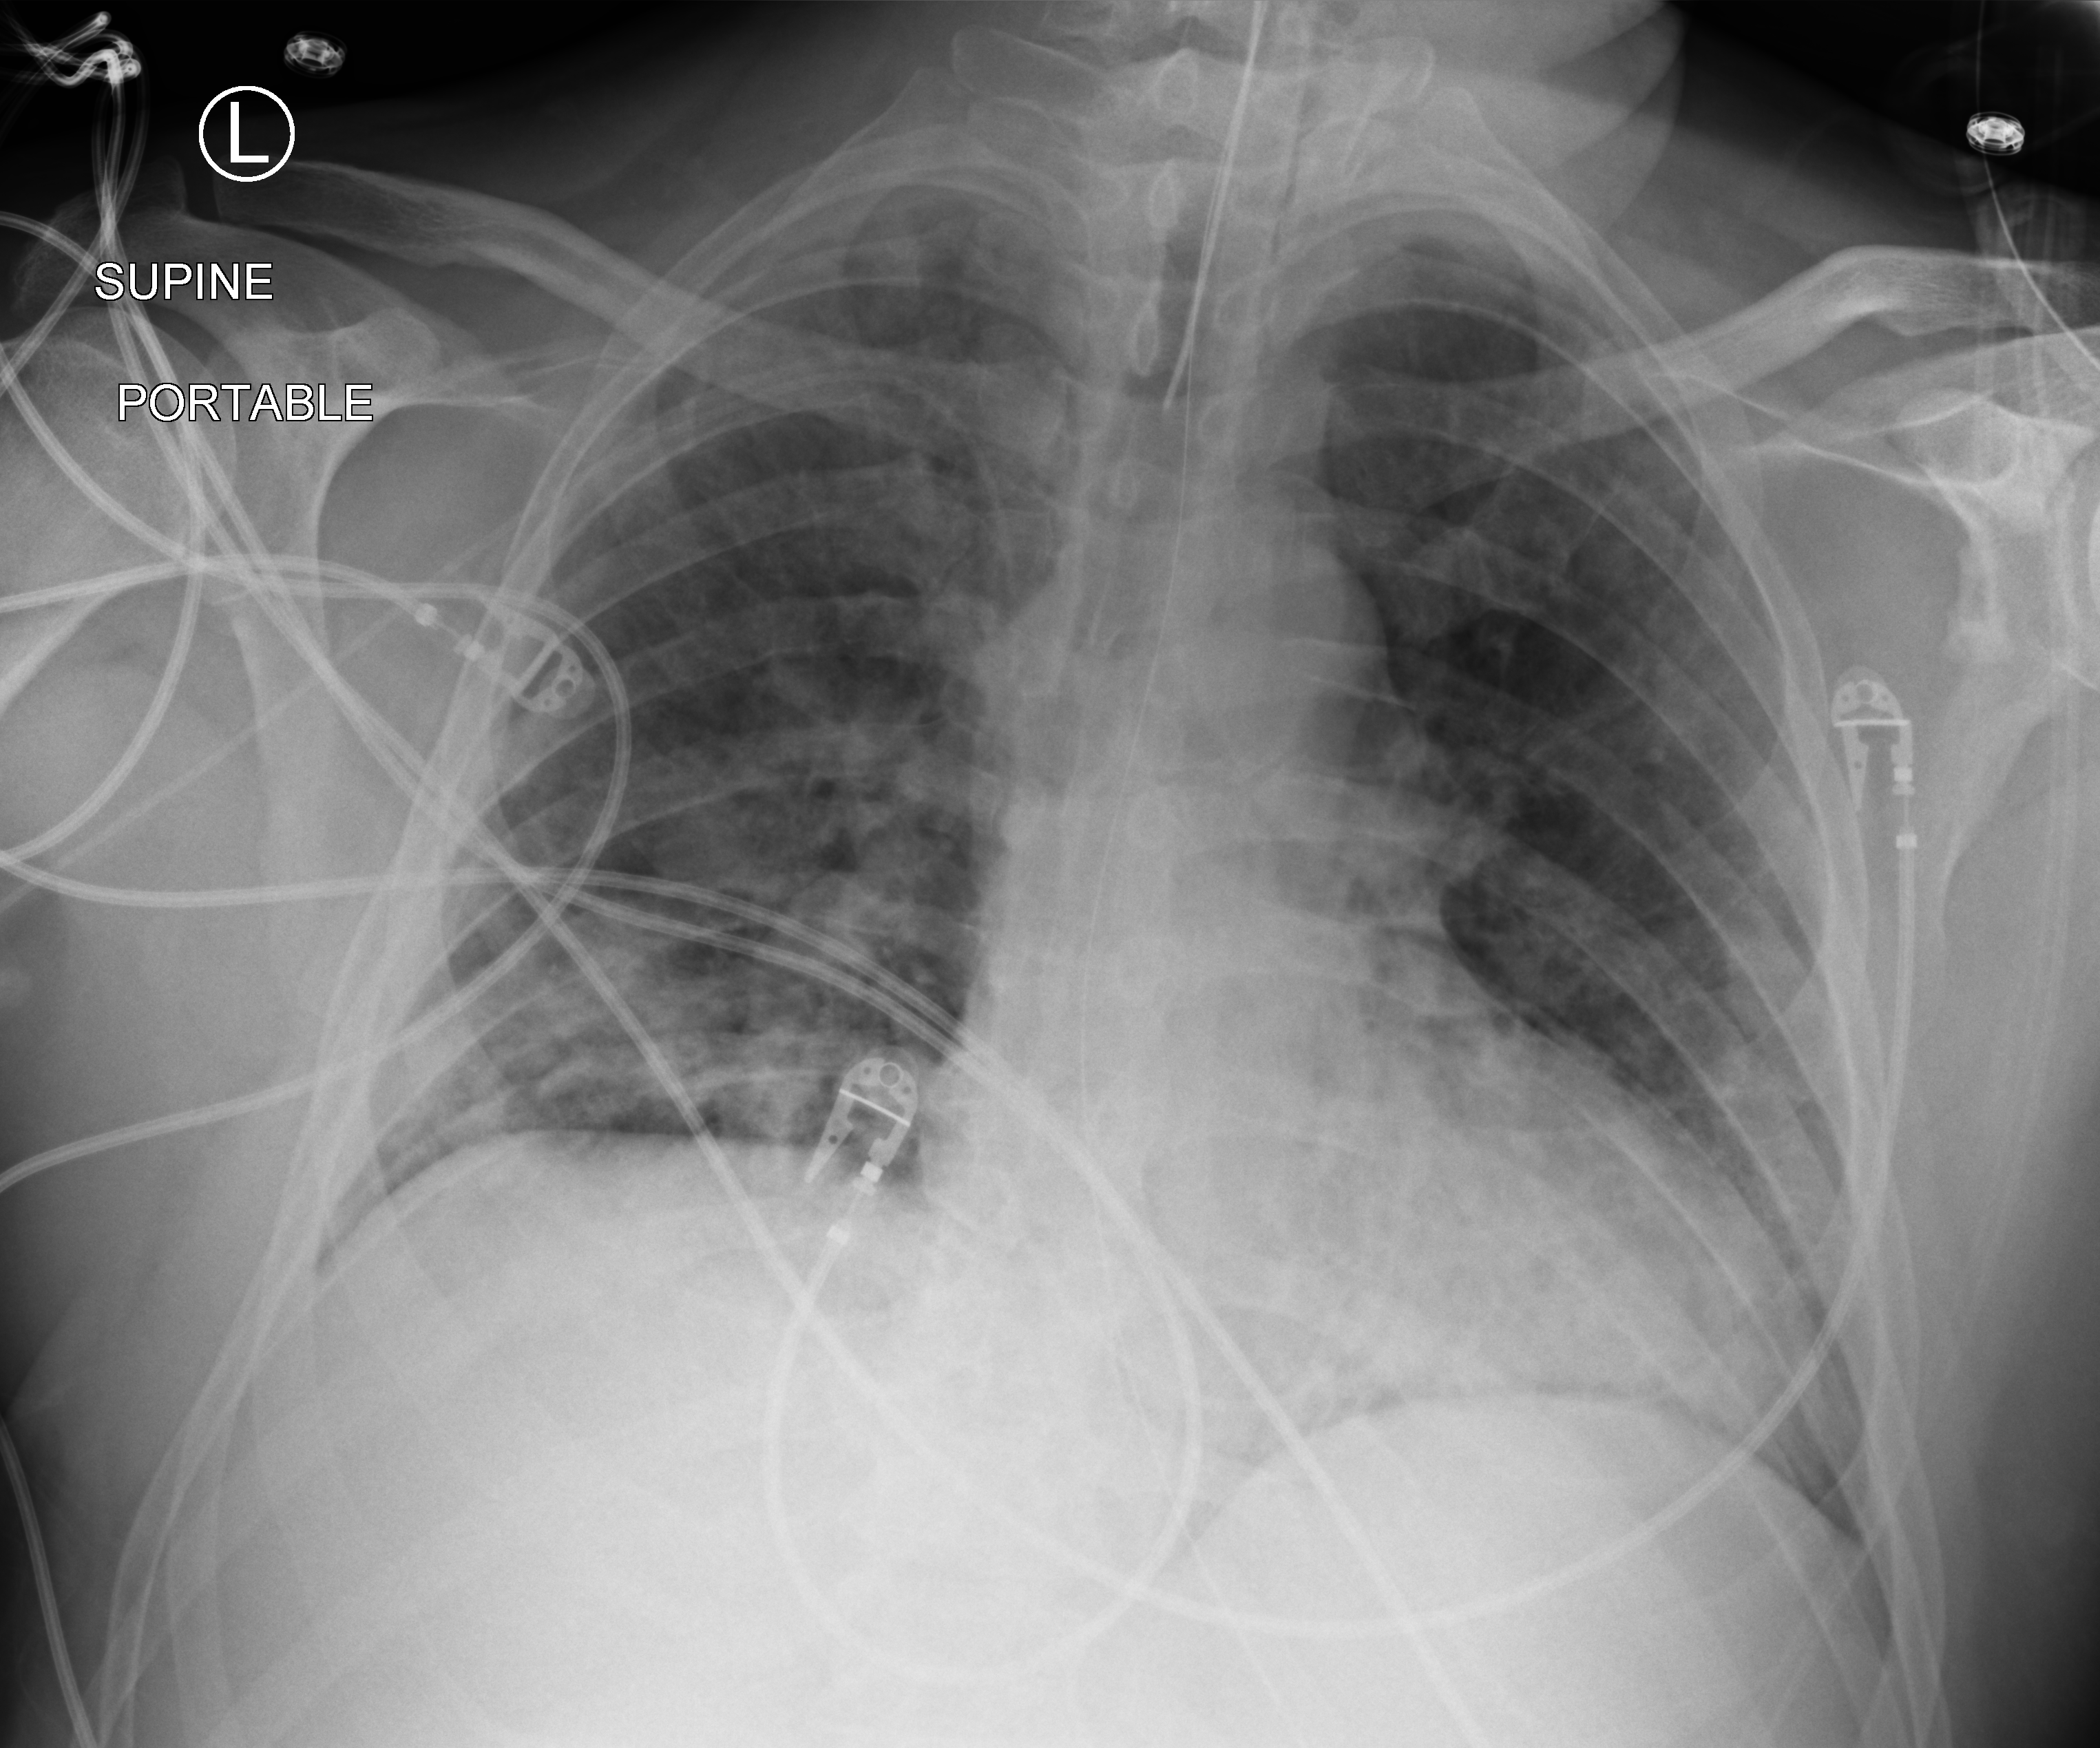
Portable chest radiograph; anteroposterior (AP) projection. Male patient hospitalised with COVID-19, age 18–59 years.
Admission-level facts for this patient (not findings on this image; timing relative to this image not recorded): admitted to intensive care during this hospital stay: no; mechanically ventilated during this hospital stay: yes.